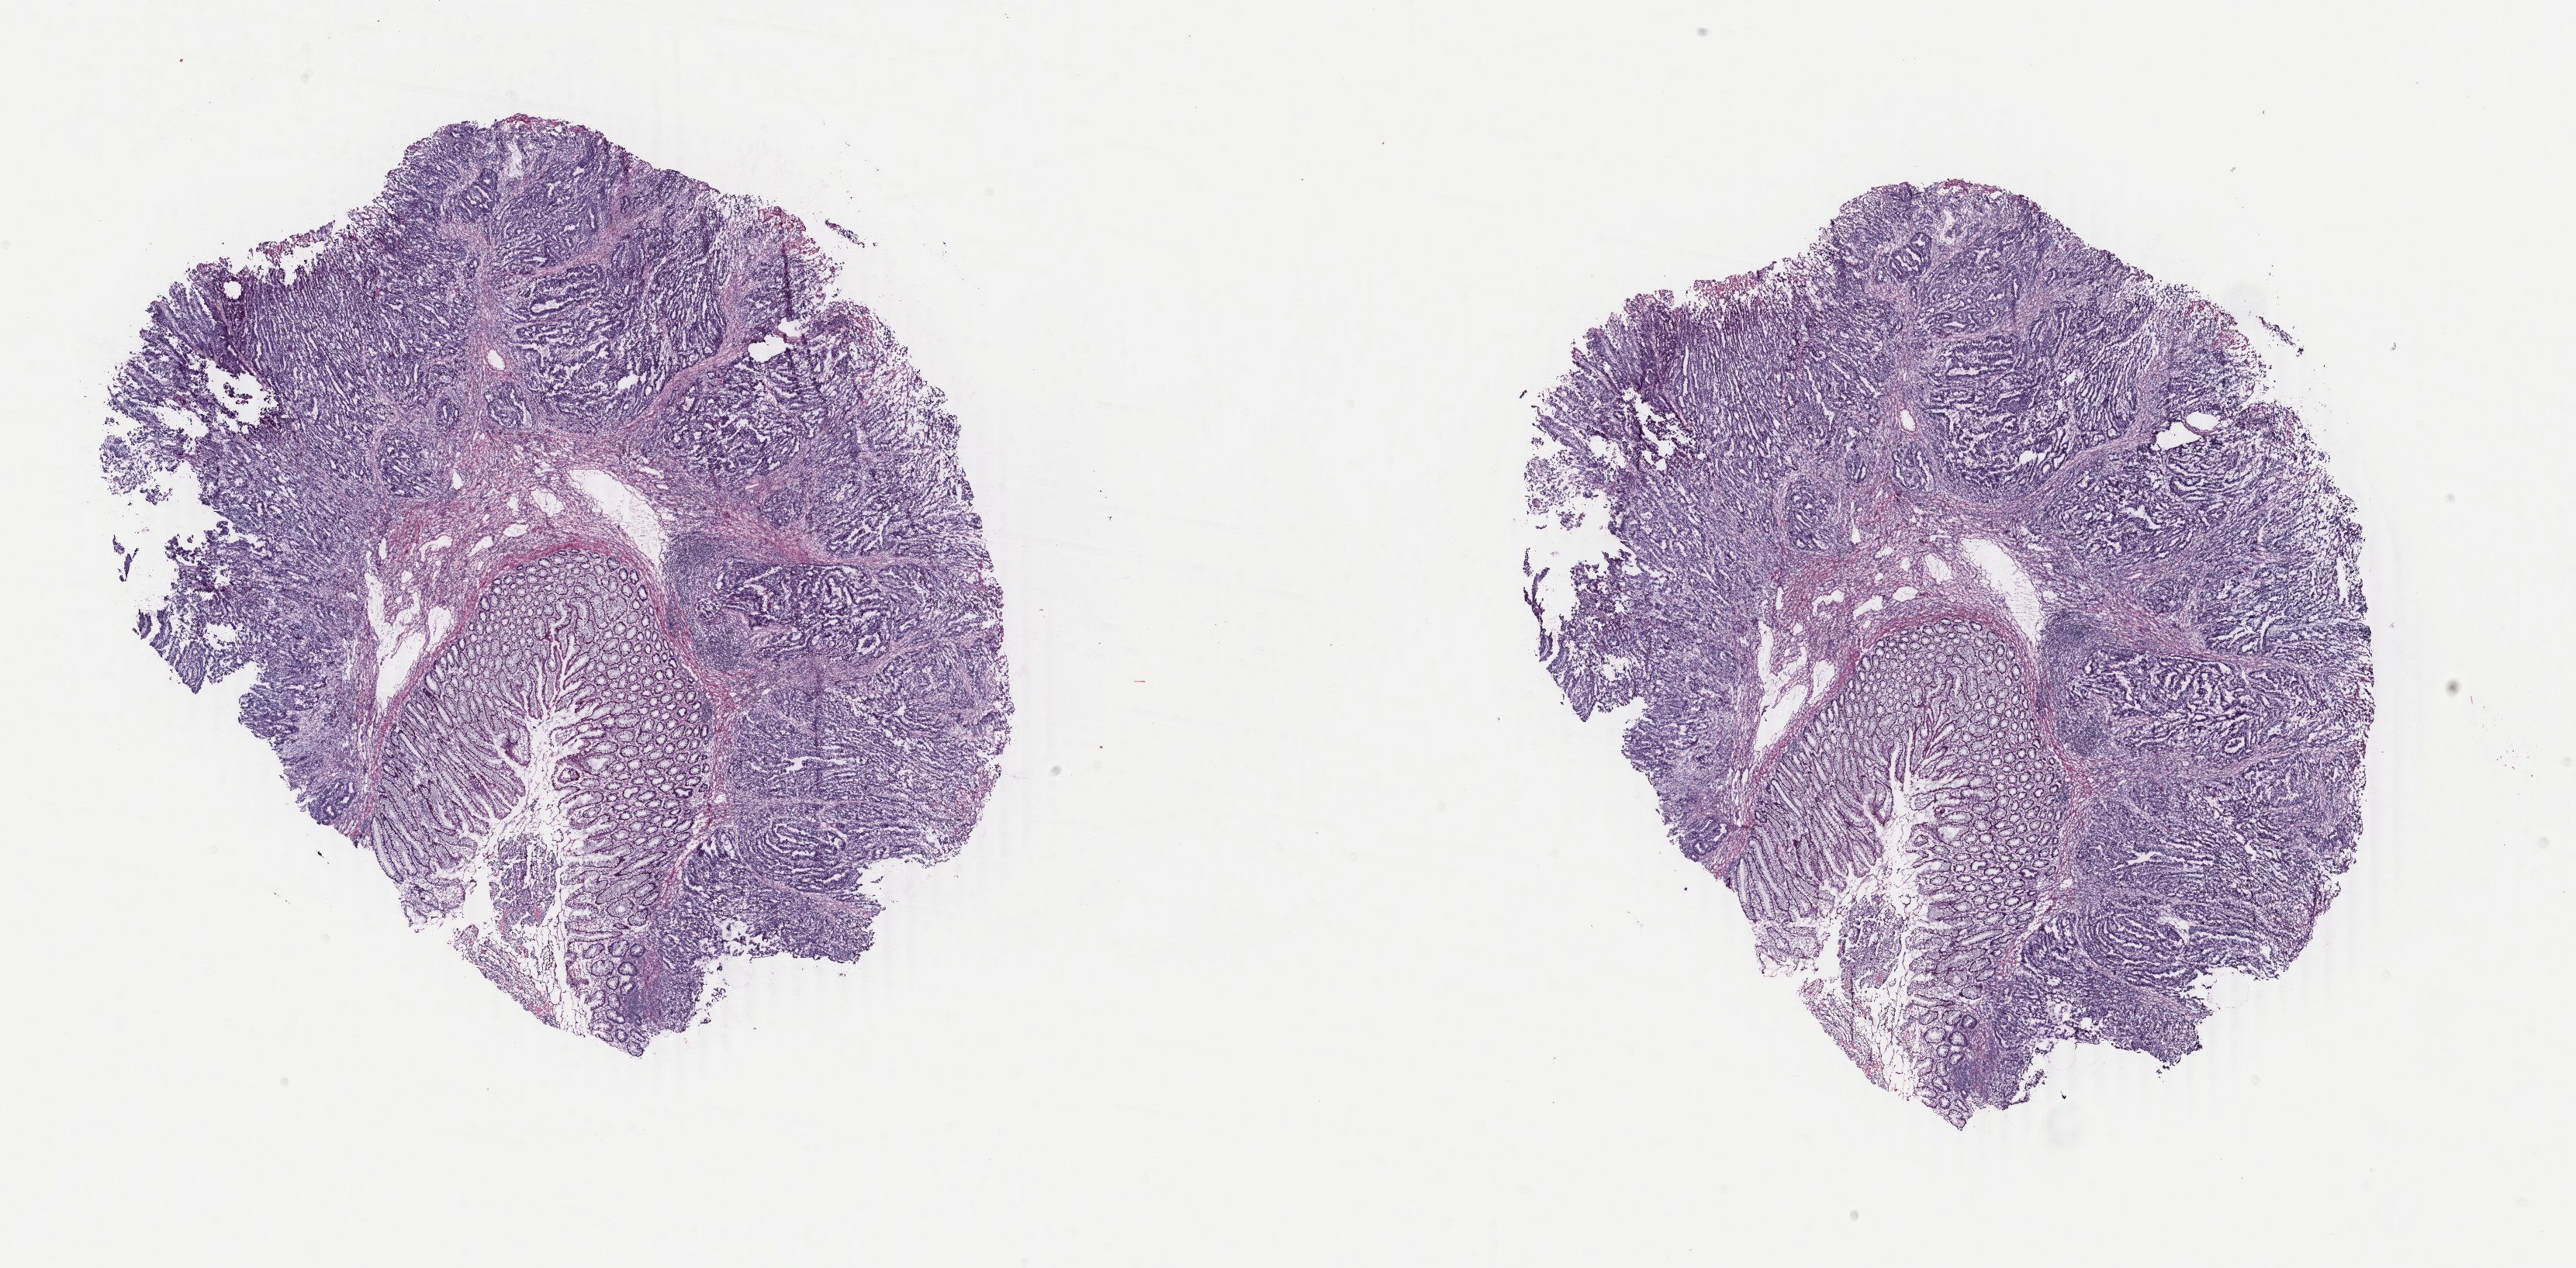
Hematoxylin and eosin (H&E) stained whole-slide image — shown as a low-resolution overview of the whole scanned area (about 26.4 x 13.0 mm, acquisition: 40x scan). Frozen section from the bottom of the tissue portion. Sample: primary tumour, rectum. Female, age 67 years at initial diagnosis. Pathologist review of this section (percent, as recorded): tumour cells 75%, tumour nuclei 75%, normal cells 12%, stromal cells 10%, necrosis 3%. Inflammatory infiltration, as recorded: lymphocyte infiltration 1%, monocyte infiltration 0%, neutrophil infiltration 12%.
- pathologic diagnosis: Adenocarcinoma, NOS
- AJCC pathologic stage: II